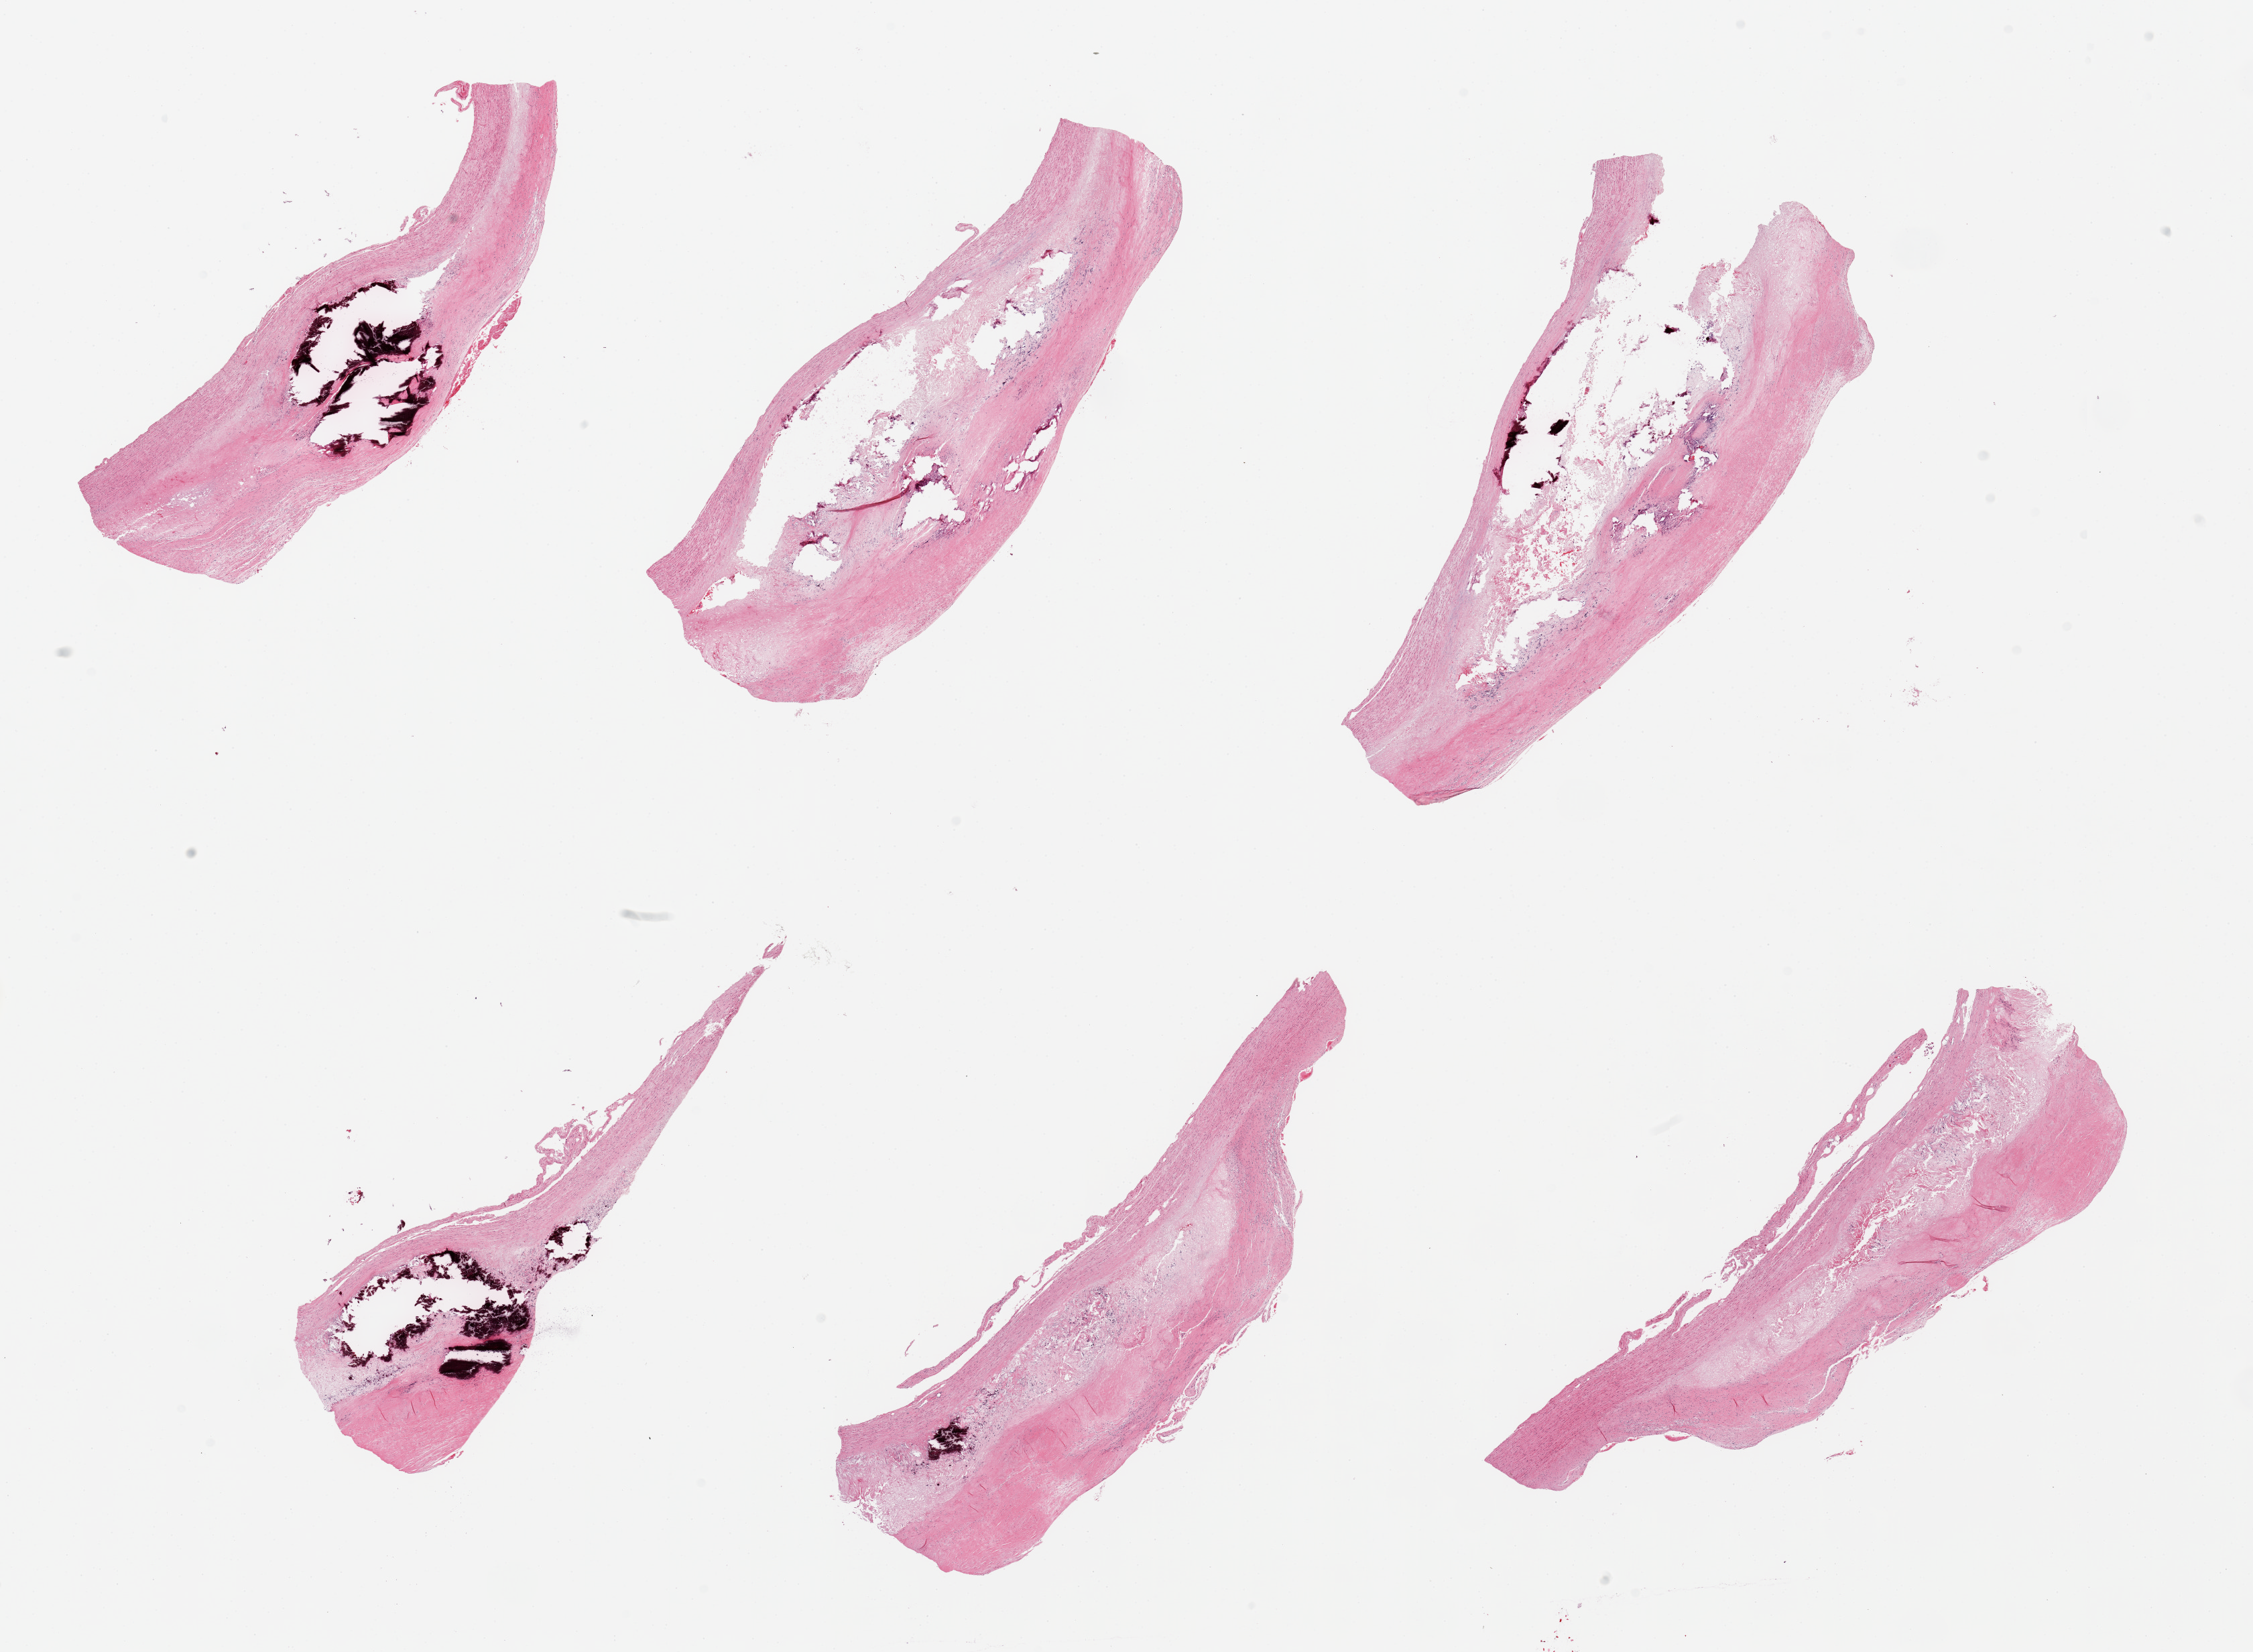
Whole-slide image, haematoxylin and eosin stain, low-resolution overview of the scanned area, about 26.6 x 19.5 mm. PAXgene-fixed paraffin-embedded (PFPE) section. Sampled site (target tissue): aorta. Donor tissue sample. Male donor.
• pathologist's review note for this sample: 6 pieces; severe calcific atherosclerosis